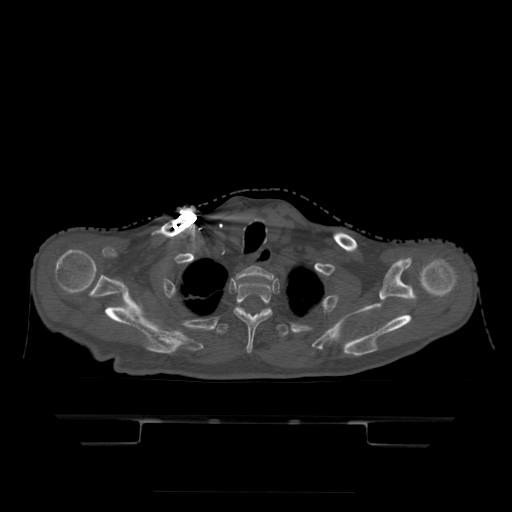
CT including the spine, one axial slice. Slice 384 of 522 in the series (ordered by position). Bone window (W 1800 / L 400 HU). 512 × 512 image matrix, field of view 436 × 436 mm. Patient age 68 years. From the clinical record (not read from this slice): primary cancer: urothelial.
Annotated regions visible in this slice (semi-automatic segmentation, software-assisted and operator-edited):
- T1 vertebra: bounding box [x1, y1, x2, y2] px = [235, 266, 273, 280]
- T2 vertebra: [234, 280, 274, 354]
- T3 vertebra: [217, 308, 287, 338]